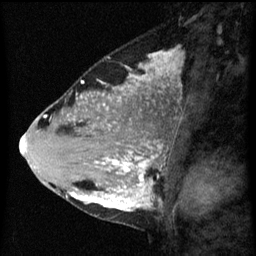
Breast MRI (dynamic contrast-enhanced), one sagittal slice. Position 25 of 60 along the scan axis. Dynamic contrast-enhanced series, image 2 of 3 at this slice position (ordered by acquisition). 1.5 T. TE 4.2 ms, TR 8 ms. 2.3 mm slice thickness. 256 × 256 image matrix, field of view 180 × 180 mm. Female patient, age 33 years.
Annotated regions visible in this slice (semi-automatic segmentation, software-assisted and operator-edited):
- analysis volume of interest (the breast-tissue region the enhancement analysis was run in; not a lesion): bounding box (x1, y1, x2, y2) in pixels: (71, 118, 168, 217)
- tumour enhancement mask (voxels above the 70 % enhancement threshold inside the analysis volume of interest): (71, 126, 161, 211)